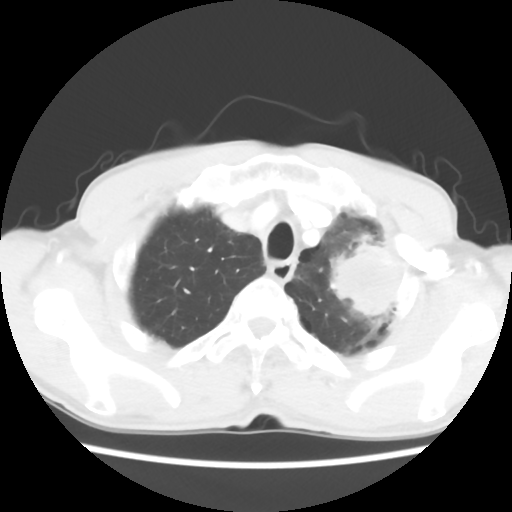
Chest CT, one axial slice; slice 51 of 60 in the series (ordered by position); 120 kVp; lung window (W 1500 / L -600 HU); 5 mm slice thickness; 512 × 512 image matrix. Male patient, age 64 years. From the clinical record (not read from this slice): clinical TNM (as recorded): T3 N3 M0.
Structures marked on this image (bounding box drawn by a radiologist):
- lung tumour (recorded histology: adenocarcinoma): box from (x=326, y=228) to (x=402, y=324) px